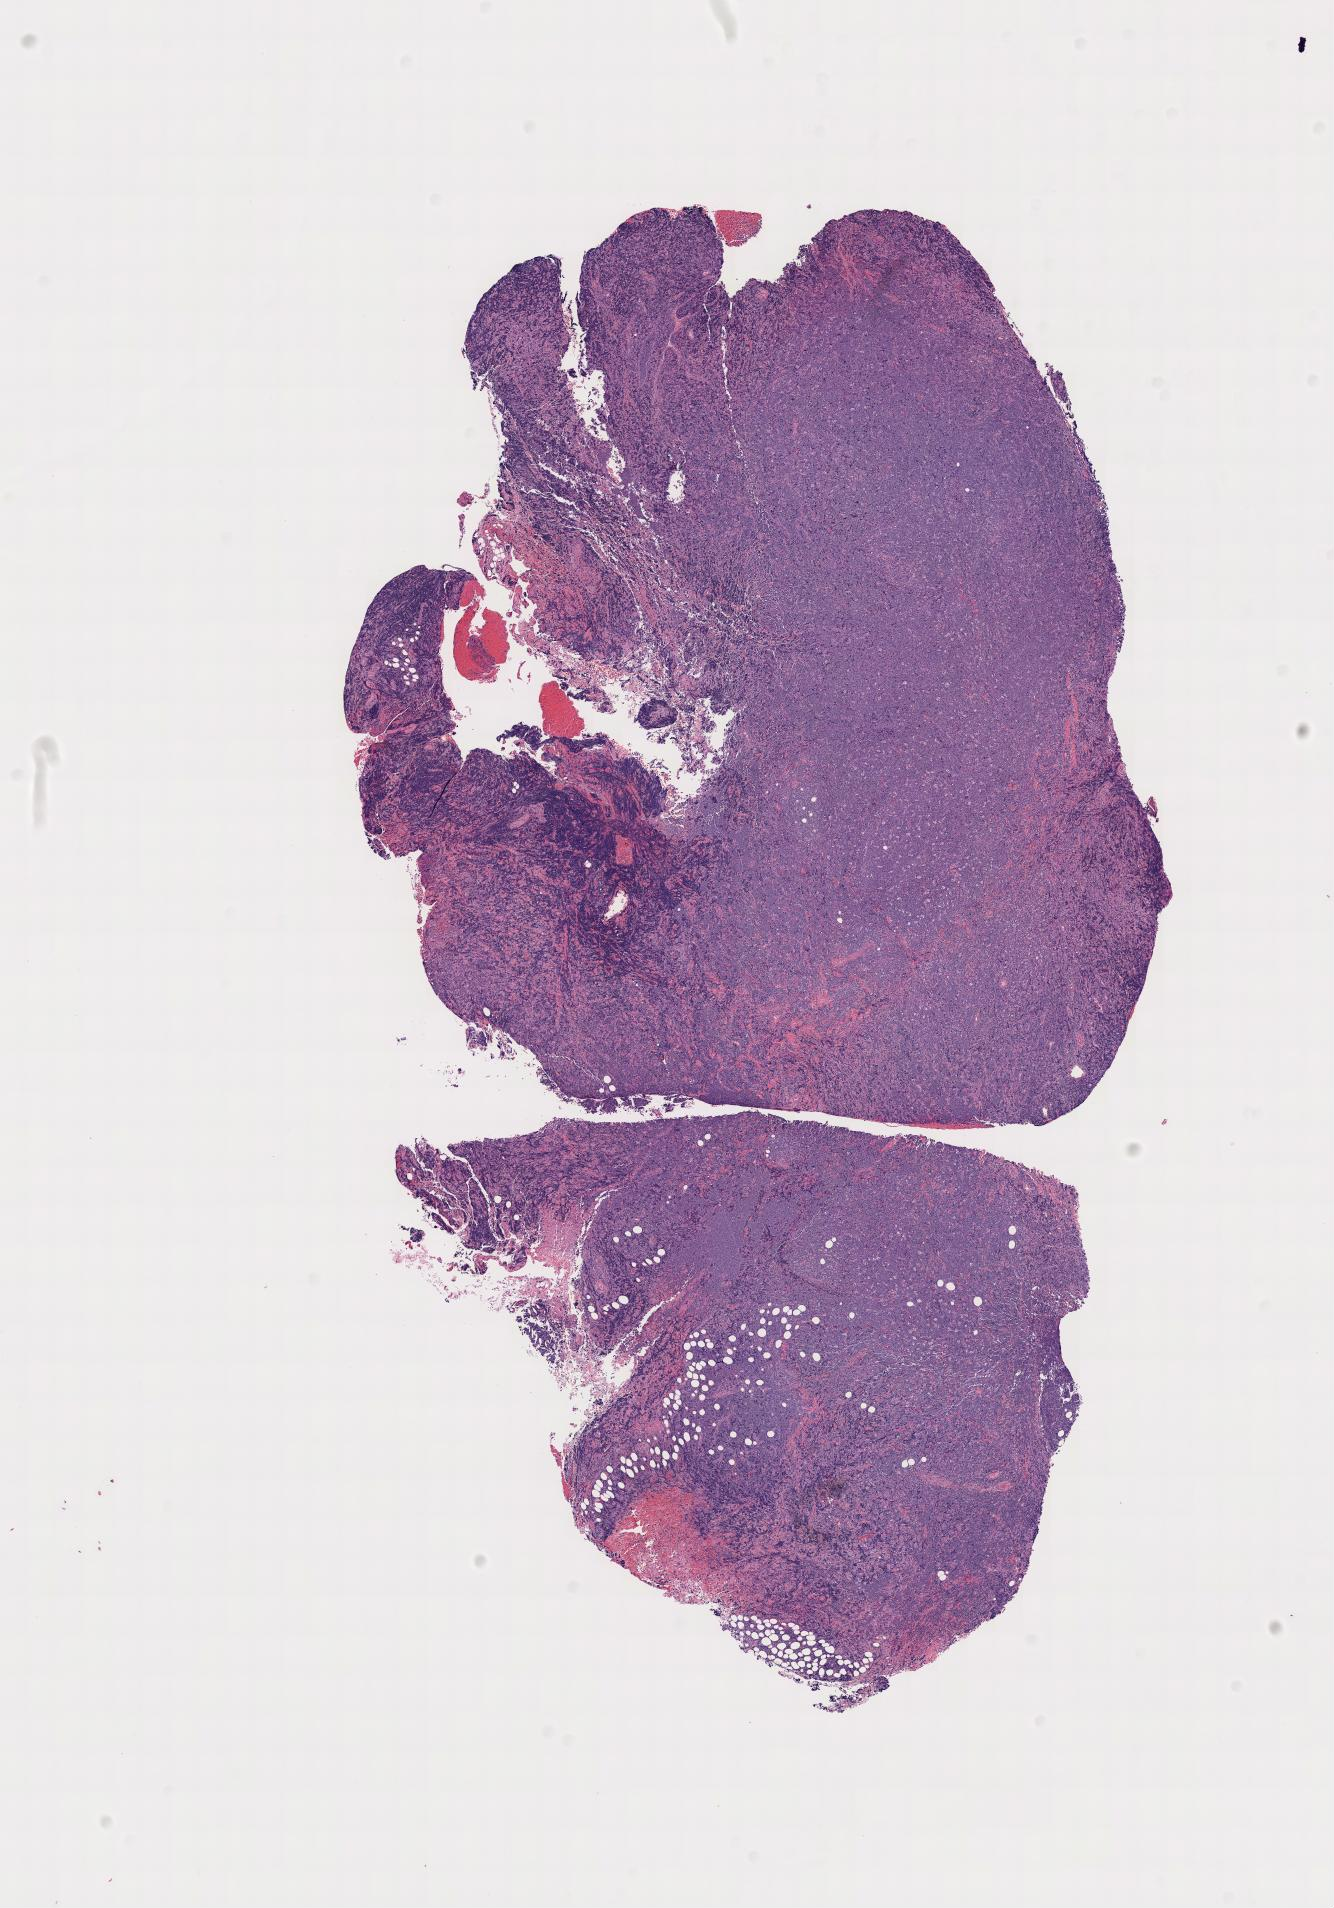
Haematoxylin and eosin whole-slide image — low-resolution overview of the scanned area, specimen: tumor tissue, anatomic site: cranium. Patient: female, age at initial diagnosis 5 years.
* histologic diagnosis: Burkitt lymphoma, NOS